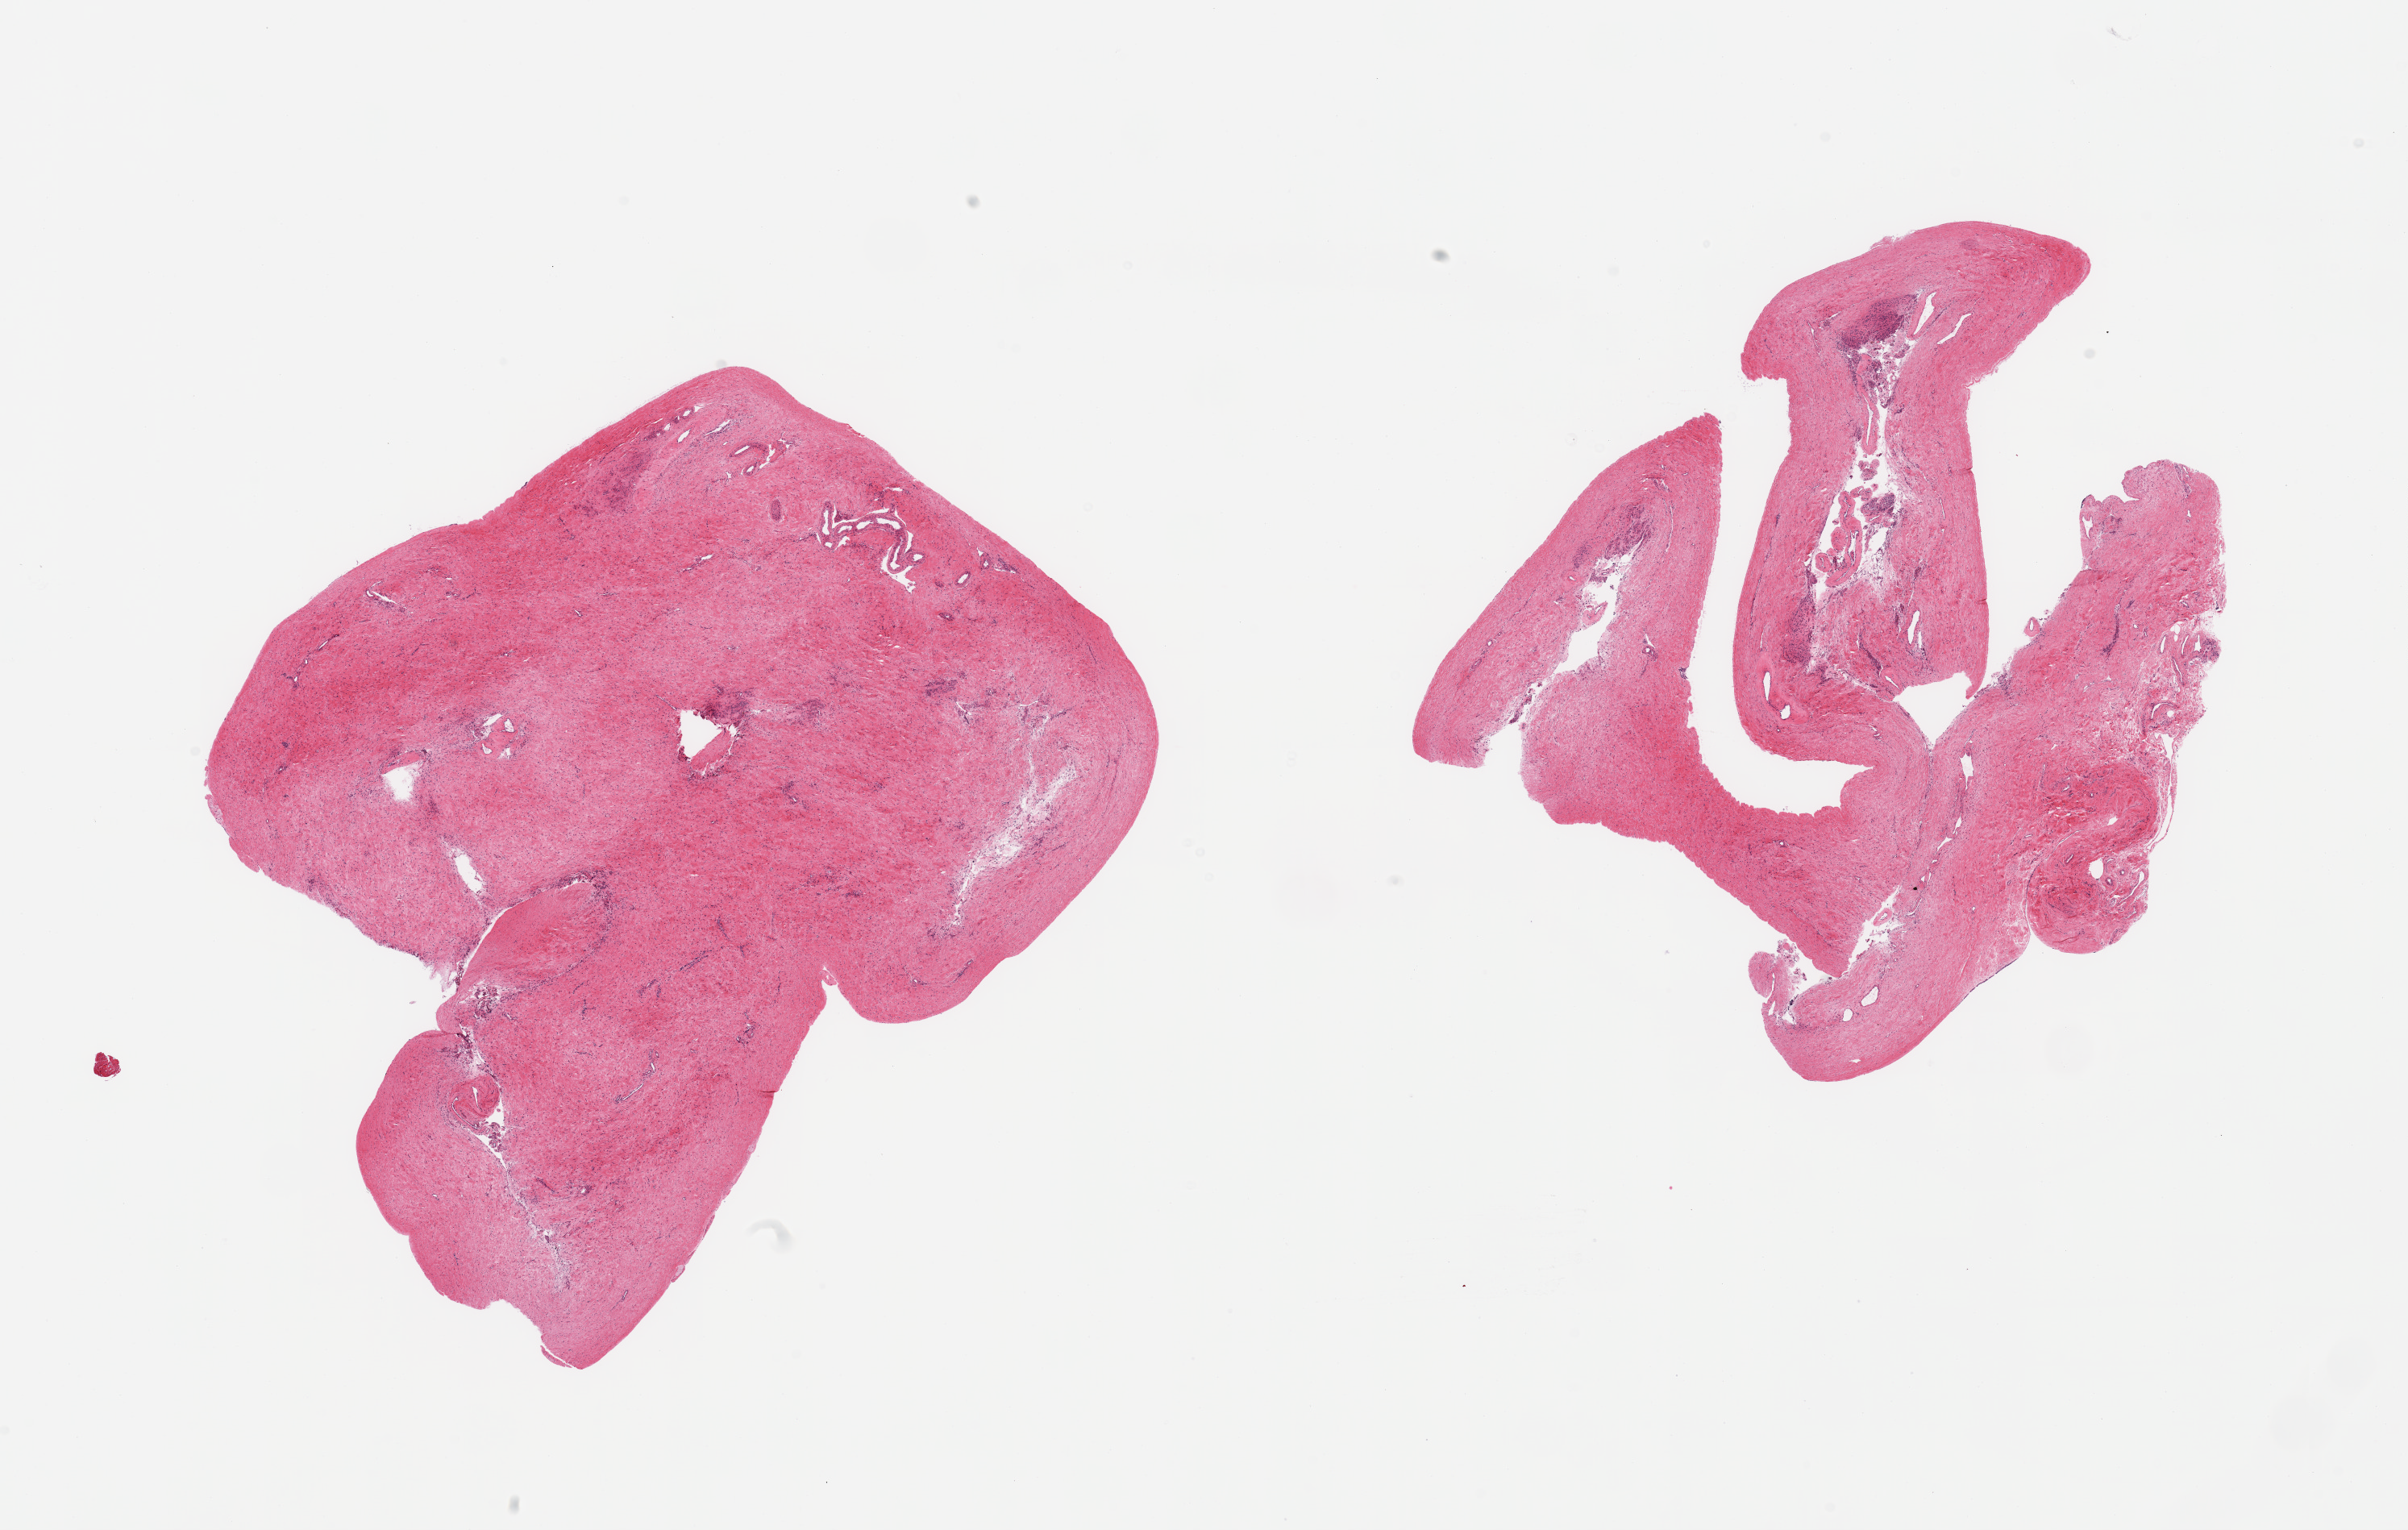
Digitized hematoxylin and eosin (H&E)-stained section, brightfield — a low-resolution overview of the entire scanned area, about 23.6 x 15.0 mm (from a 20x scan). PAXgene-fixed paraffin-embedded (PFPE) section. Section of testis (target tissue). Tissue donor sample. Donor: male.
- reviewer comment on this tissue sample: 2 pieces, dense hyaline tissue, trace seminiferous tubules/Leydig cells, suspect fibrotic process, insufficient target tissue